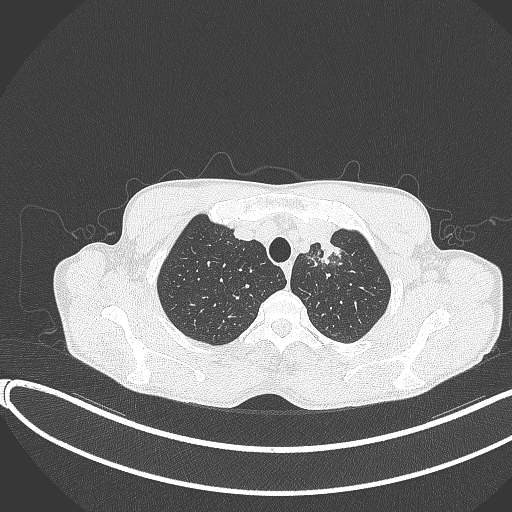
Chest CT, one axial slice; slice 331 of 374 in the series (ordered by position); reconstruction kernel B70f; 120 kVp; lung window (W 1500 / L -600 HU); 512 × 512 image matrix, field of view 400 × 400 mm. Patient: male, 58 years. From the clinical record (not read from this slice): clinical TNM (as recorded): T1c N1 M0.
Annotated regions visible in this slice (bounding box drawn by a radiologist):
- lung tumour (recorded histology: adenocarcinoma): bounding box <316,232,343,264> (left, top, right, bottom; pixels)